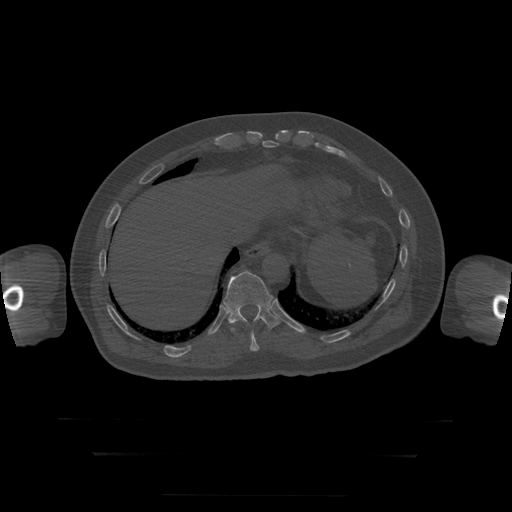
CT including the spine, one axial slice. Position 108 of 397 along the scan axis. 120 kVp. Bone window (W 1800 / L 400 HU). 1.25 mm slice thickness. 512 × 512 image matrix, field of view 510 × 510 mm. Patient age 73 years. From the clinical record (not read from this slice): primary cancer: prostate.
Outlined on this slice (semi-automatically segmented with operator editing):
- T10 vertebra: bounding box <250,331,260,352> (left, top, right, bottom; pixels)
- T11 vertebra: <223,271,281,332>